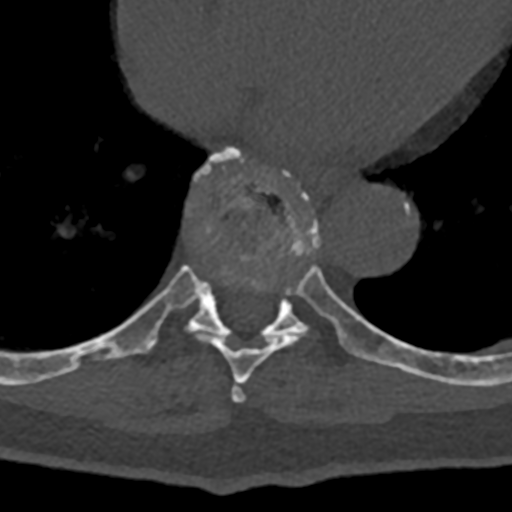
CT including the spine, one axial slice. Slice 683 of 797 in the series (ordered by position). Bone window (W 1800 / L 400 HU). 512 × 512 image matrix, field of view 160 × 160 mm. Patient: male, 74 years. From the clinical record (not read from this slice): primary cancer: renal.
Outlined on this slice (semi-automatic segmentation, software-assisted and operator-edited):
- T7 vertebra: bounding box <231,383,245,402> (left, top, right, bottom; pixels)
- T8 vertebra: <70,173,344,384>
- T9 vertebra: <81,148,432,378>